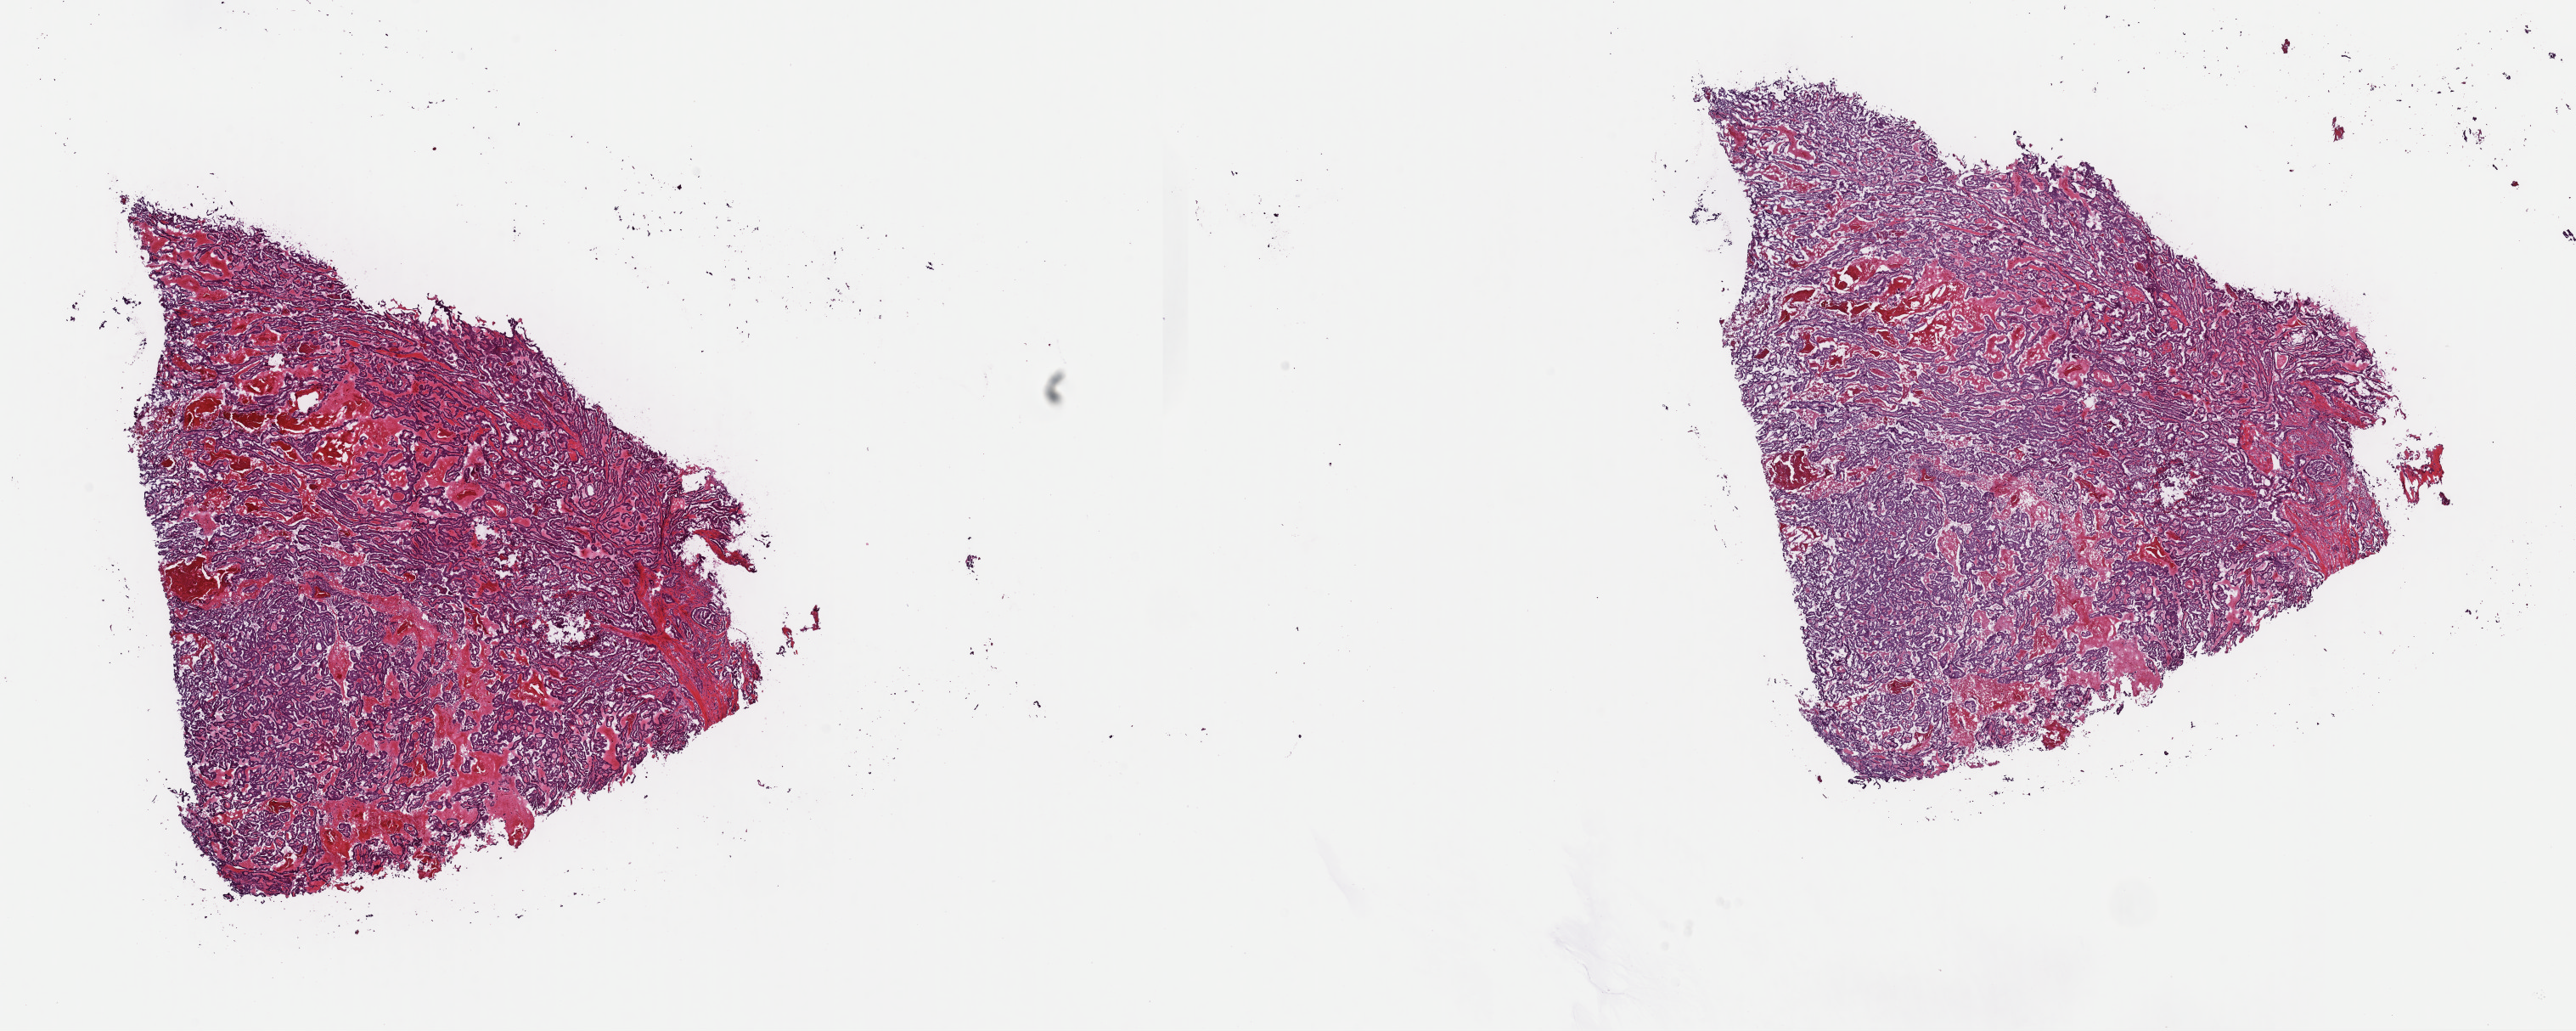
H&E-stained whole-slide image, low-resolution overview of the scanned area, about 24.0 x 9.6 mm (acquisition: 40x scan), frozen section from the top of the tissue portion, primary tumour sample from the thyroid. Male patient; age at initial diagnosis 52 years. Slide review estimates, as recorded: tumour cells 85%, tumour nuclei 85%, normal cells 0%, stromal cells 15%, necrosis 0%. Inflammatory infiltration, as recorded: lymphocyte infiltration 1%, monocyte infiltration 0%, neutrophil infiltration 0%.
• histologic diagnosis: Papillary adenocarcinoma, NOS
• AJCC pathologic stage: III (7th edition)
• lymph nodes positive (case pathology): 7 of 7 examined